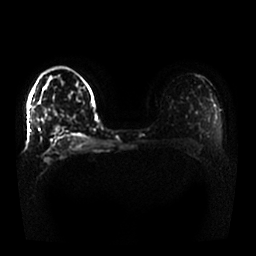
Breast MRI, one axial slice; slice 12 of 25 in the series (ordered by position); diffusion-weighted series; image 2 of 4 stored at this slice position (different b-values; order by instance number); 1.5 T; 4 mm slice thickness; 256 × 256 image matrix, field of view 370 × 370 mm. Female patient.
Outlined on this slice (manually delineated by an expert):
- tumour on diffusion-weighted imaging: box from (x=55, y=127) to (x=64, y=132) px